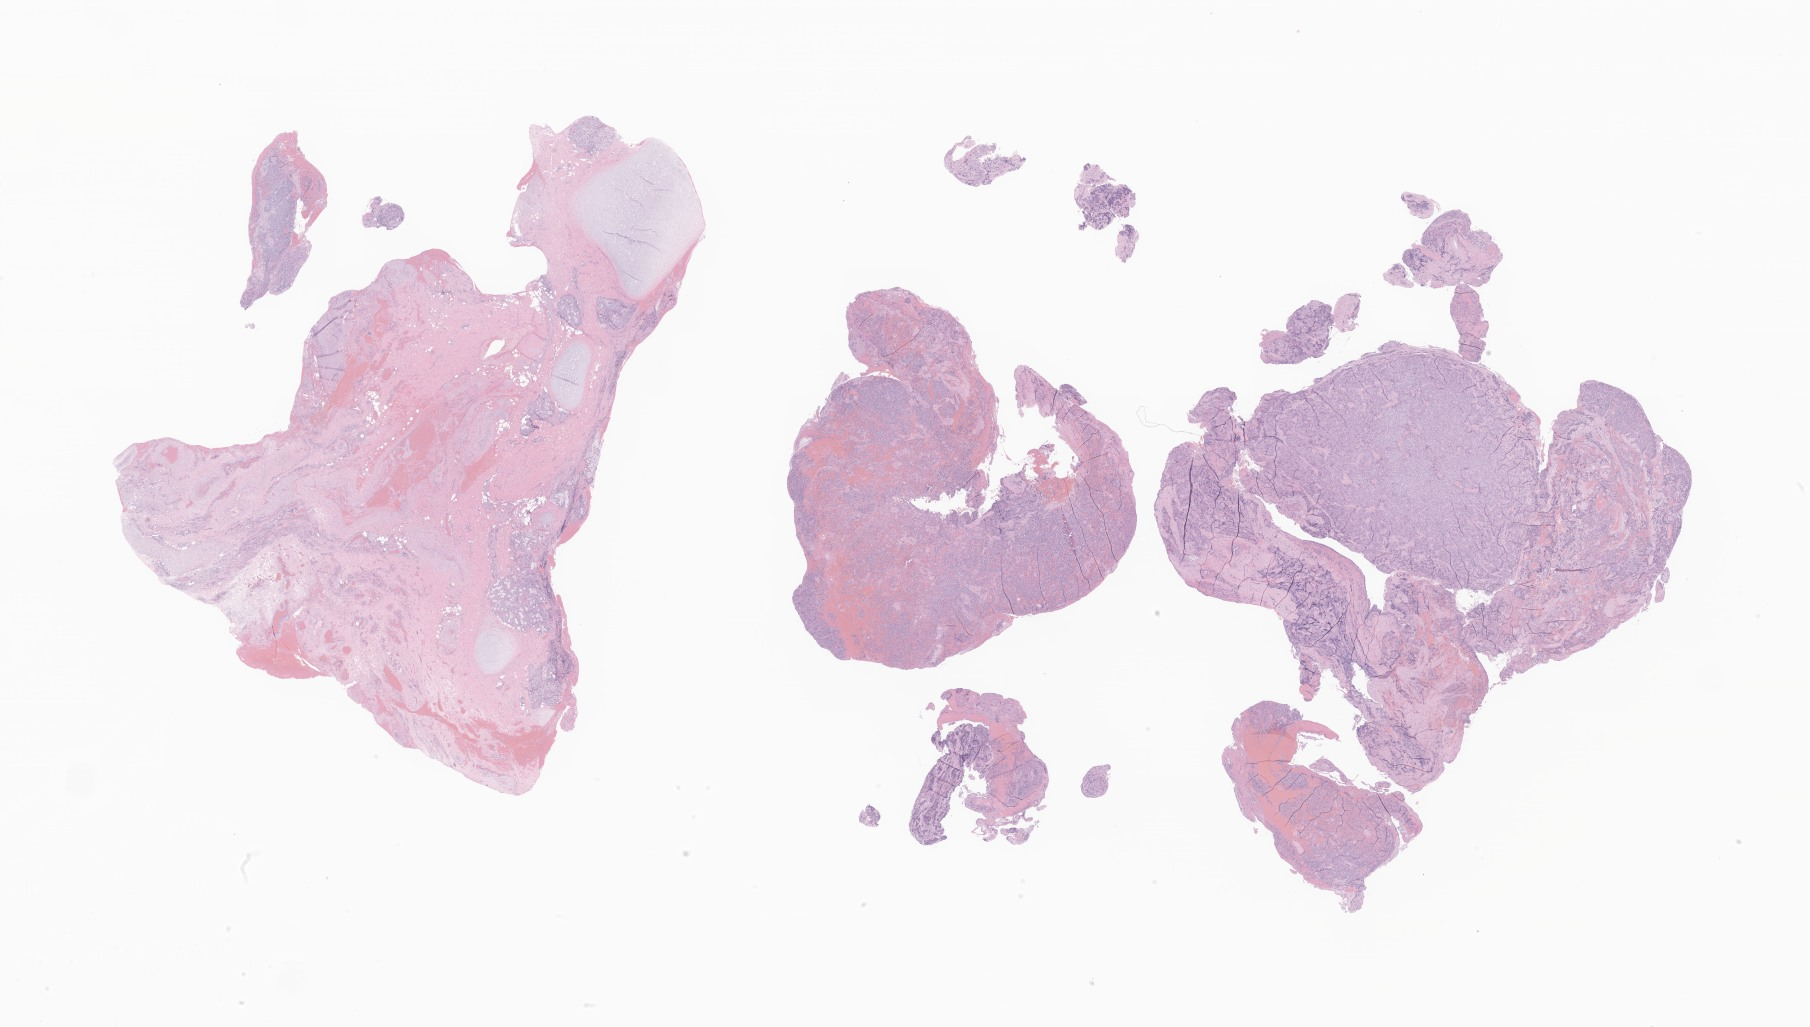
Digitized H&E-stained section of tumor tissue from the upper lobe of lung — a low-resolution overview of the entire scanned area, about 30.5 x 17.3 mm. Formalin-fixed paraffin-embedded section. Patient female; age 190 months.
Tissue or organ of origin (case record): upper lobe, lung. Diagnosis: Neuroendocrine tumor, NOS.